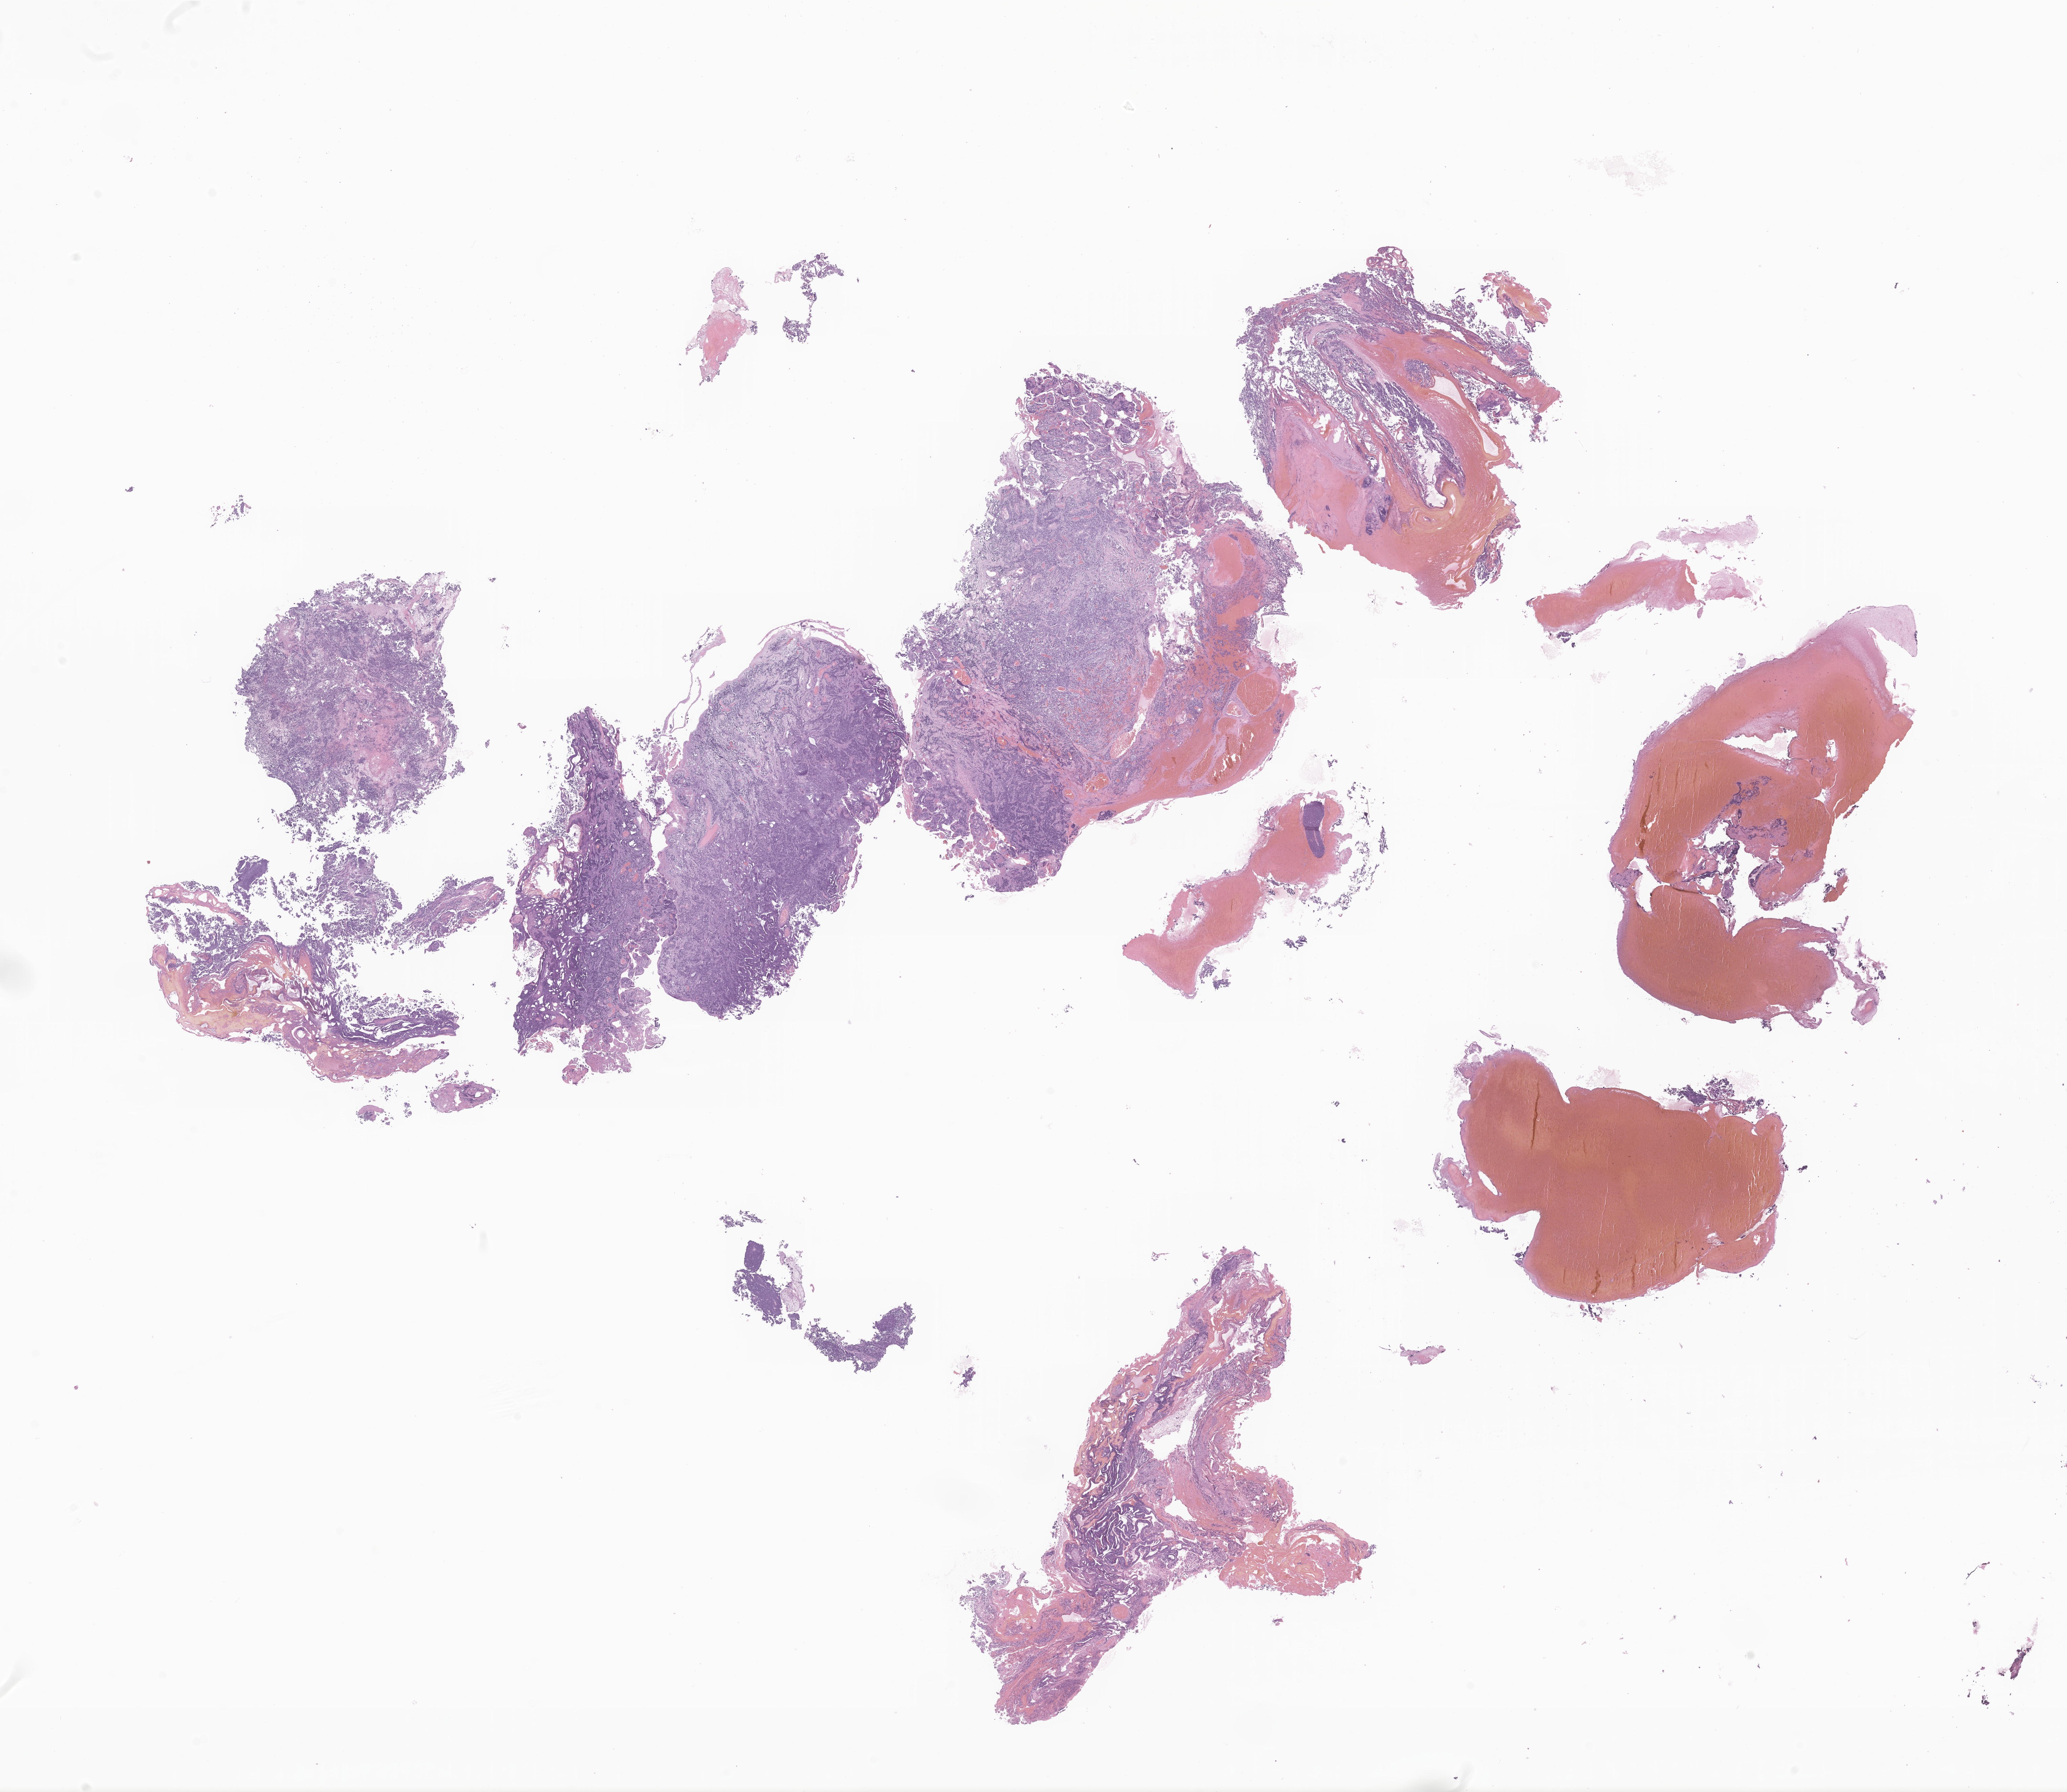
Digitized hematoxylin and eosin (H&E)-stained section of tumor tissue from the brain — shown as a low-resolution overview of the whole scanned area (about 25.7 x 22.3 mm), formalin-fixed, paraffin-embedded (FFPE) tissue. Patient: male, age 184 months (15 years 4 months).
- diagnosis: Medulloblastoma, NOS